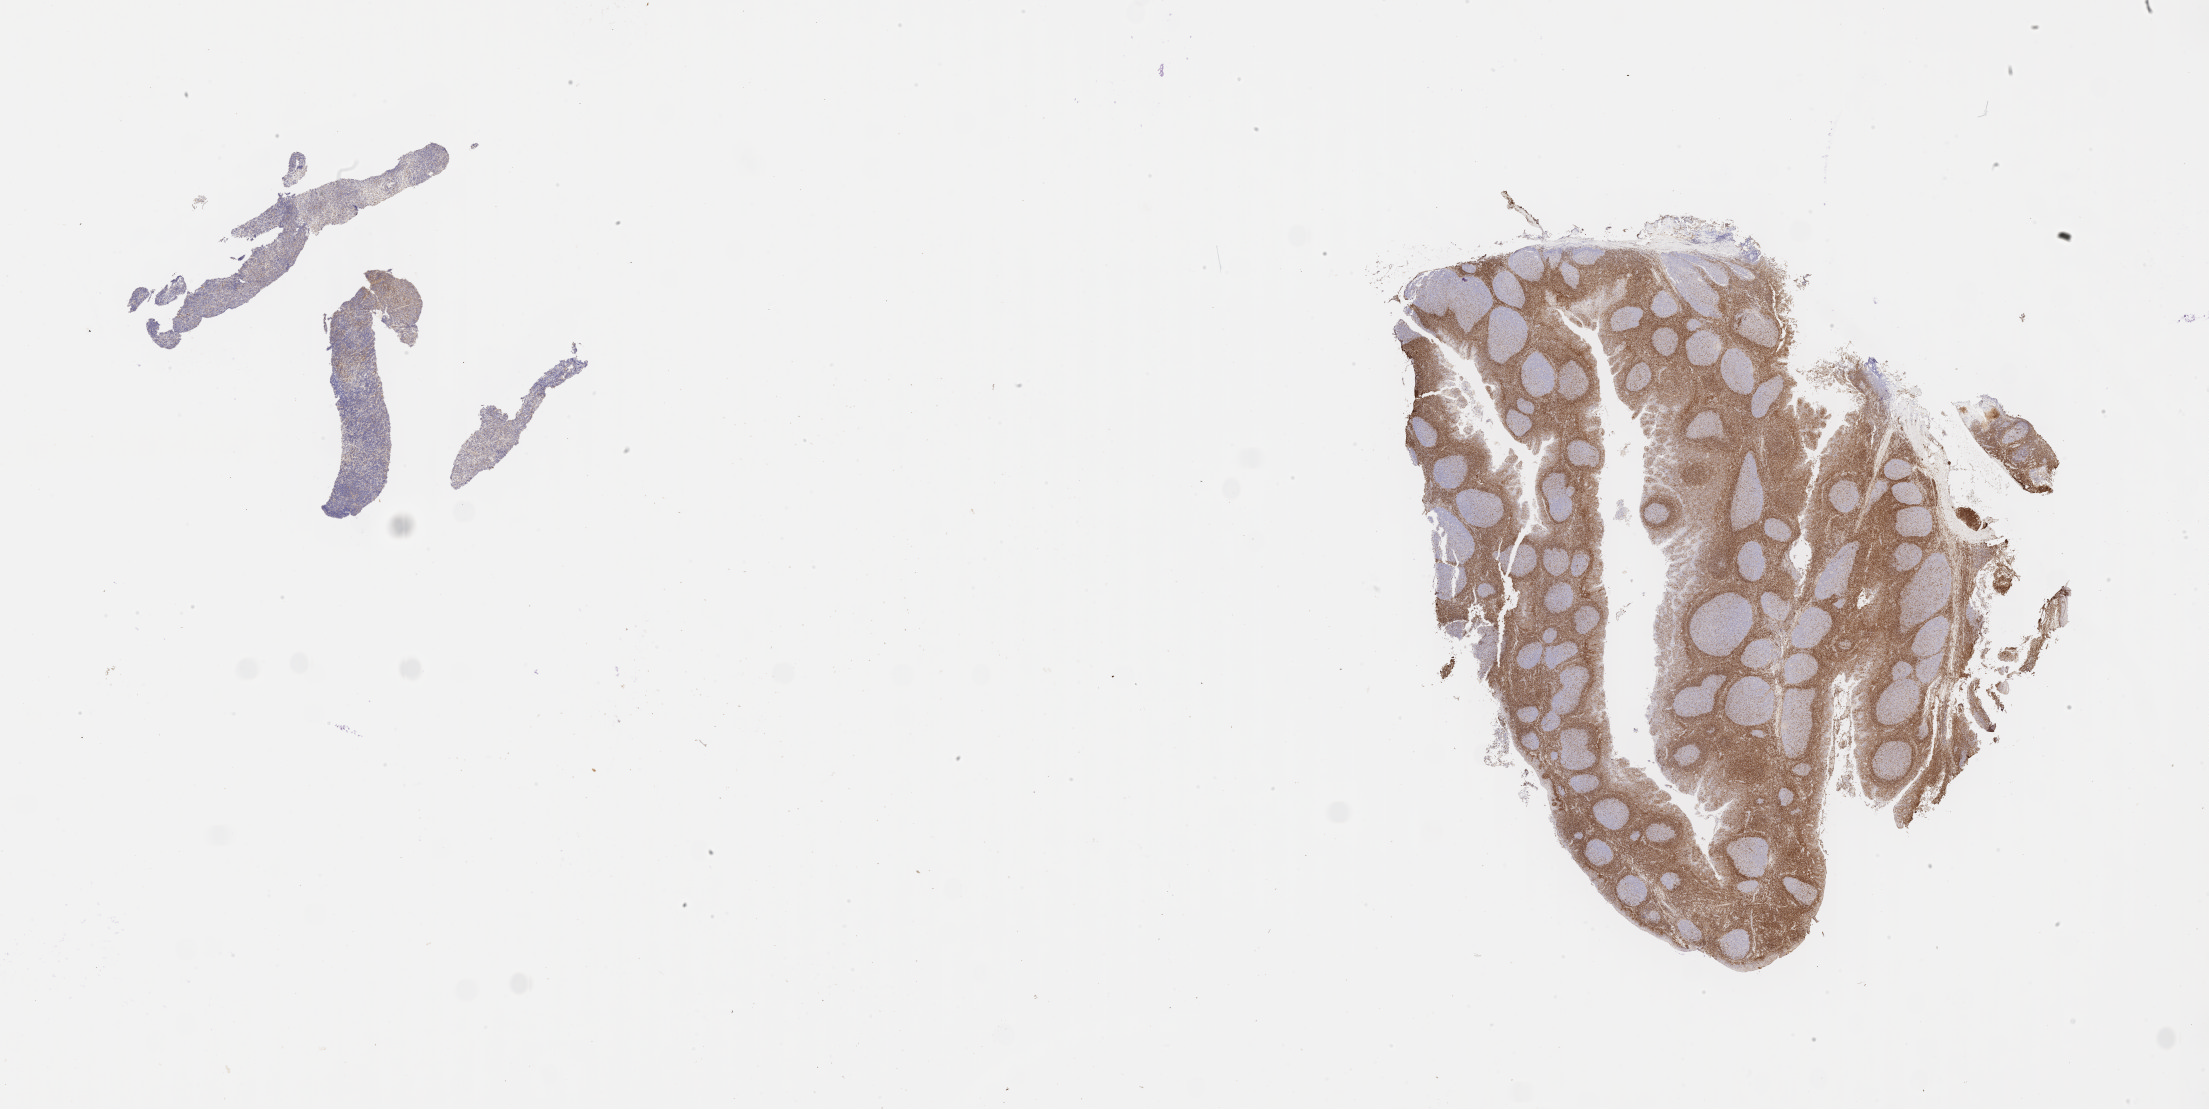
IHC for BCL2, whole-slide image, a low-resolution overview of the entire scanned area, about 35.7 x 17.9 mm, tumor tissue, site: abdomen proper. Male, age 2 years at initial diagnosis.
• histologic diagnosis: Diffuse large B-cell lymphoma, NOS